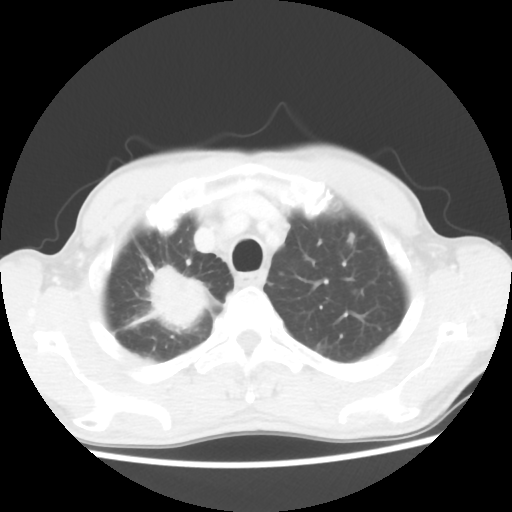
Chest CT, one axial slice; slice 44 of 52 in the series (ordered by position); 100 kVp; lung window (W 1500 / L -600 HU); 5 mm slice thickness; 512 × 512 image matrix, field of view 323 × 323 mm. Patient: male, 66 years. From the clinical record (not read from this slice): clinical TNM (as recorded): T2 N0 M1a.
Structures marked on this image (bounding box drawn by a radiologist):
- lung tumour (recorded histology: adenocarcinoma): bounding box [x1, y1, x2, y2] px = [136, 265, 225, 331]